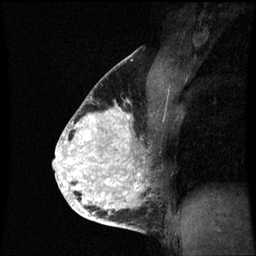
Breast MRI (dynamic contrast-enhanced), one sagittal slice; slice 40 of 60 in the series (ordered by position); dynamic contrast-enhanced series, image 2 of 3 at this slice position (ordered by acquisition); 1.5 T; TE 4.2 ms, TR 8.9 ms; 2 mm slice thickness; 256 × 256 image matrix, field of view 200 × 200 mm. Patient: female, 35 years. From the clinical record (not read from this slice): setting: breast cancer imaged before/during neoadjuvant chemotherapy; receptor status: HR-positive, HER2-negative.
Outlined on this slice (semi-automatically segmented with operator editing):
- analysis volume of interest (the breast-tissue region the enhancement analysis was run in; not a lesion): bounding box <66,100,159,215> (left, top, right, bottom; pixels)
- tumour enhancement mask (voxels above the 70 % enhancement threshold inside the analysis volume of interest): <66,106,149,215>